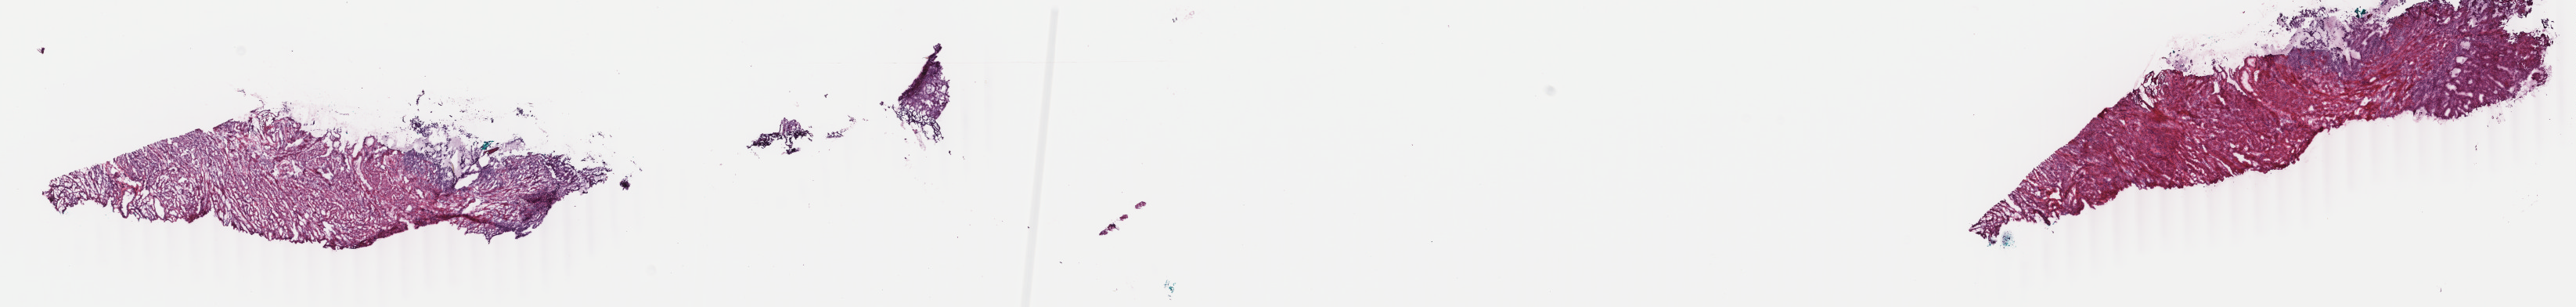
Hematoxylin and eosin (H&E) stained whole-slide image — whole scanned area (about 26.2 x 3.1 mm, acquisition: 40x scan) shown as a low-resolution overview; frozen section; uterus, primary tumour sample. Patient: female, age at initial diagnosis 54 years. Histologic grade: G1 (well differentiated). Pathologist review of this section (percent, as recorded): tumour cells 100%, tumour nuclei 75%, normal cells 0%, stromal cells 0%, necrosis 0%. Inflammatory infiltration, as recorded: lymphocyte infiltration 0%, monocyte infiltration 0%, neutrophil infiltration 0%.
Histologic diagnosis: Endometrioid adenocarcinoma, NOS (endometrium). FIGO stage: IA.